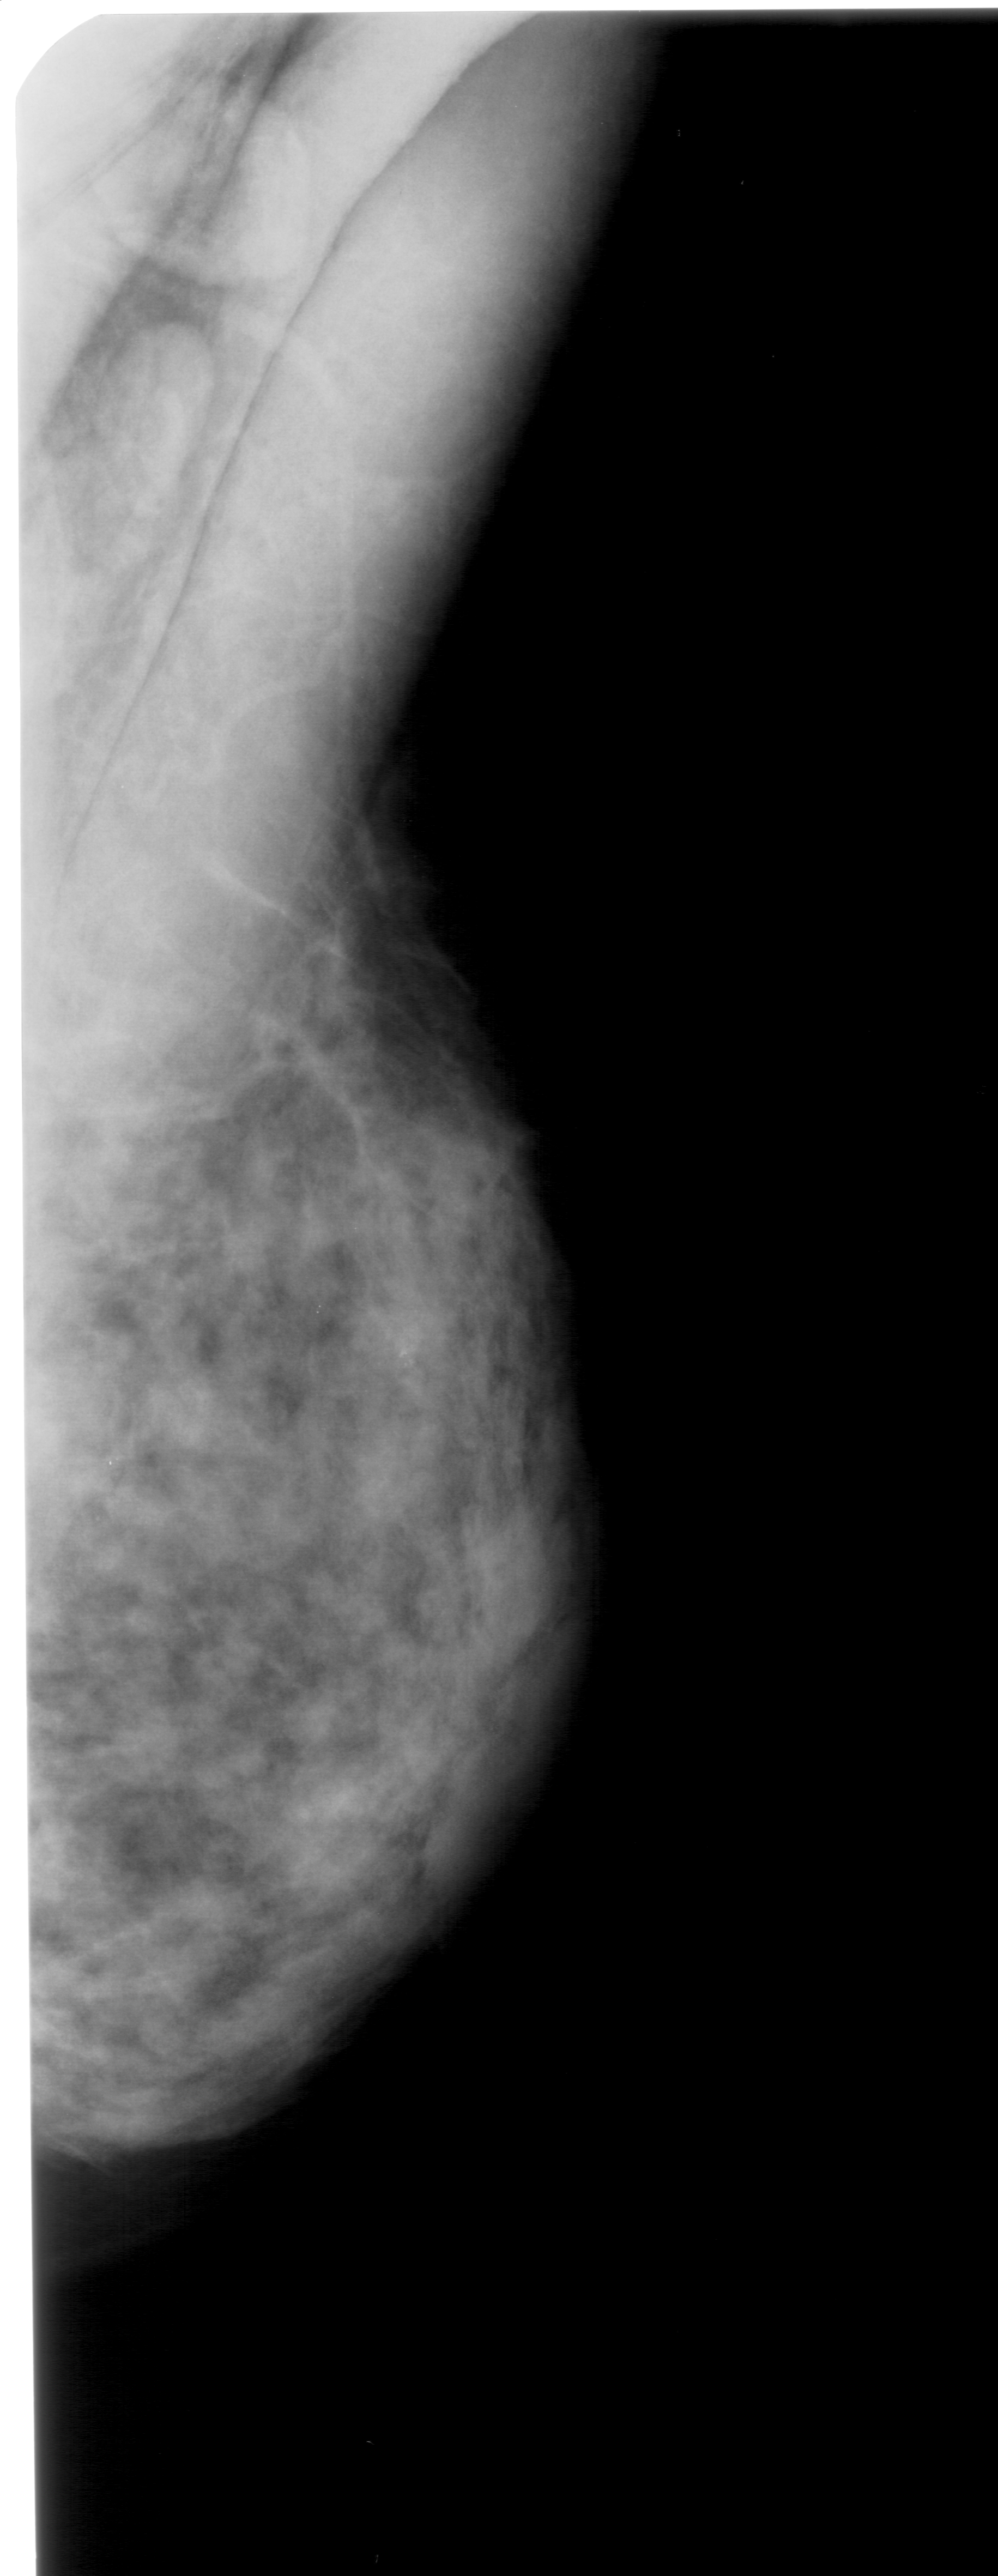
Mammogram (digitized film); right breast; MLO view; 998 × 2576 image matrix.
Expert-marked regions of interest on this film, with their recorded descriptors:
- calcifications, morphology pleomorphic, distribution clustered; BI-RADS assessment category 4; subtlety rating 3 on a 1 (subtle) to 5 (obvious) scale; pathology (as recorded): benign: bounding box (x1, y1, x2, y2) in pixels: (371, 1328, 446, 1414)